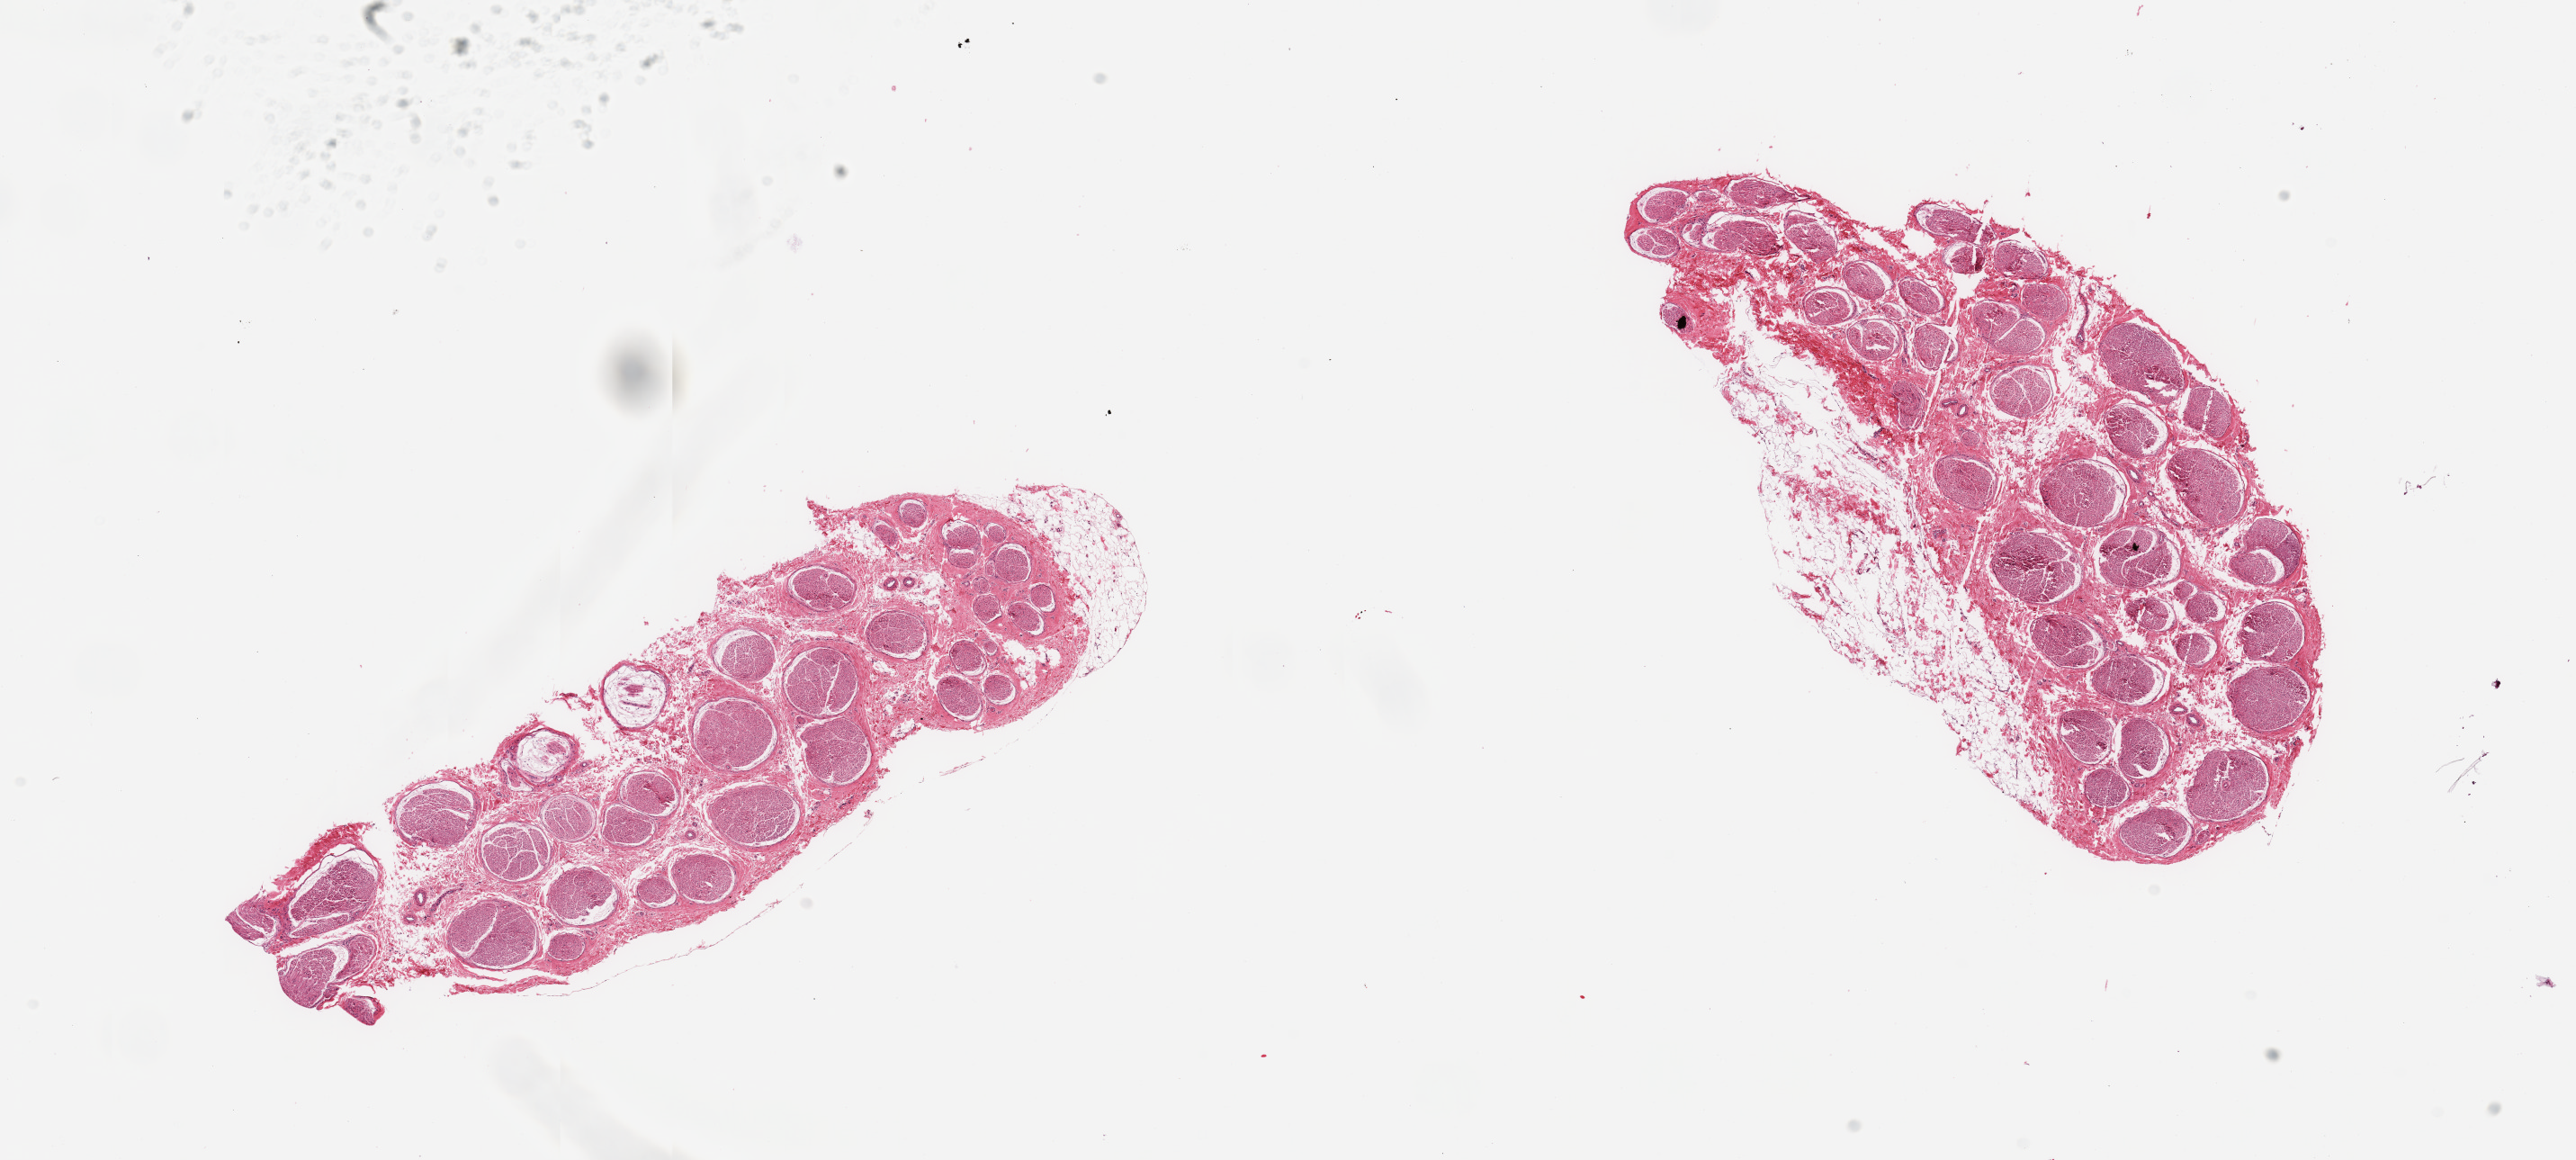
Digitized H&E-stained section, a low-resolution overview of the entire scanned area, about 22.6 x 10.2 mm (from a 20x scan), PAXgene-fixed paraffin-embedded (PFPE) section, sampled site (target tissue): tibial nerve, donor tissue sample.
• reviewer comment on this tissue sample: 2 pieces, trace nubbins of fat, ~0.5mm